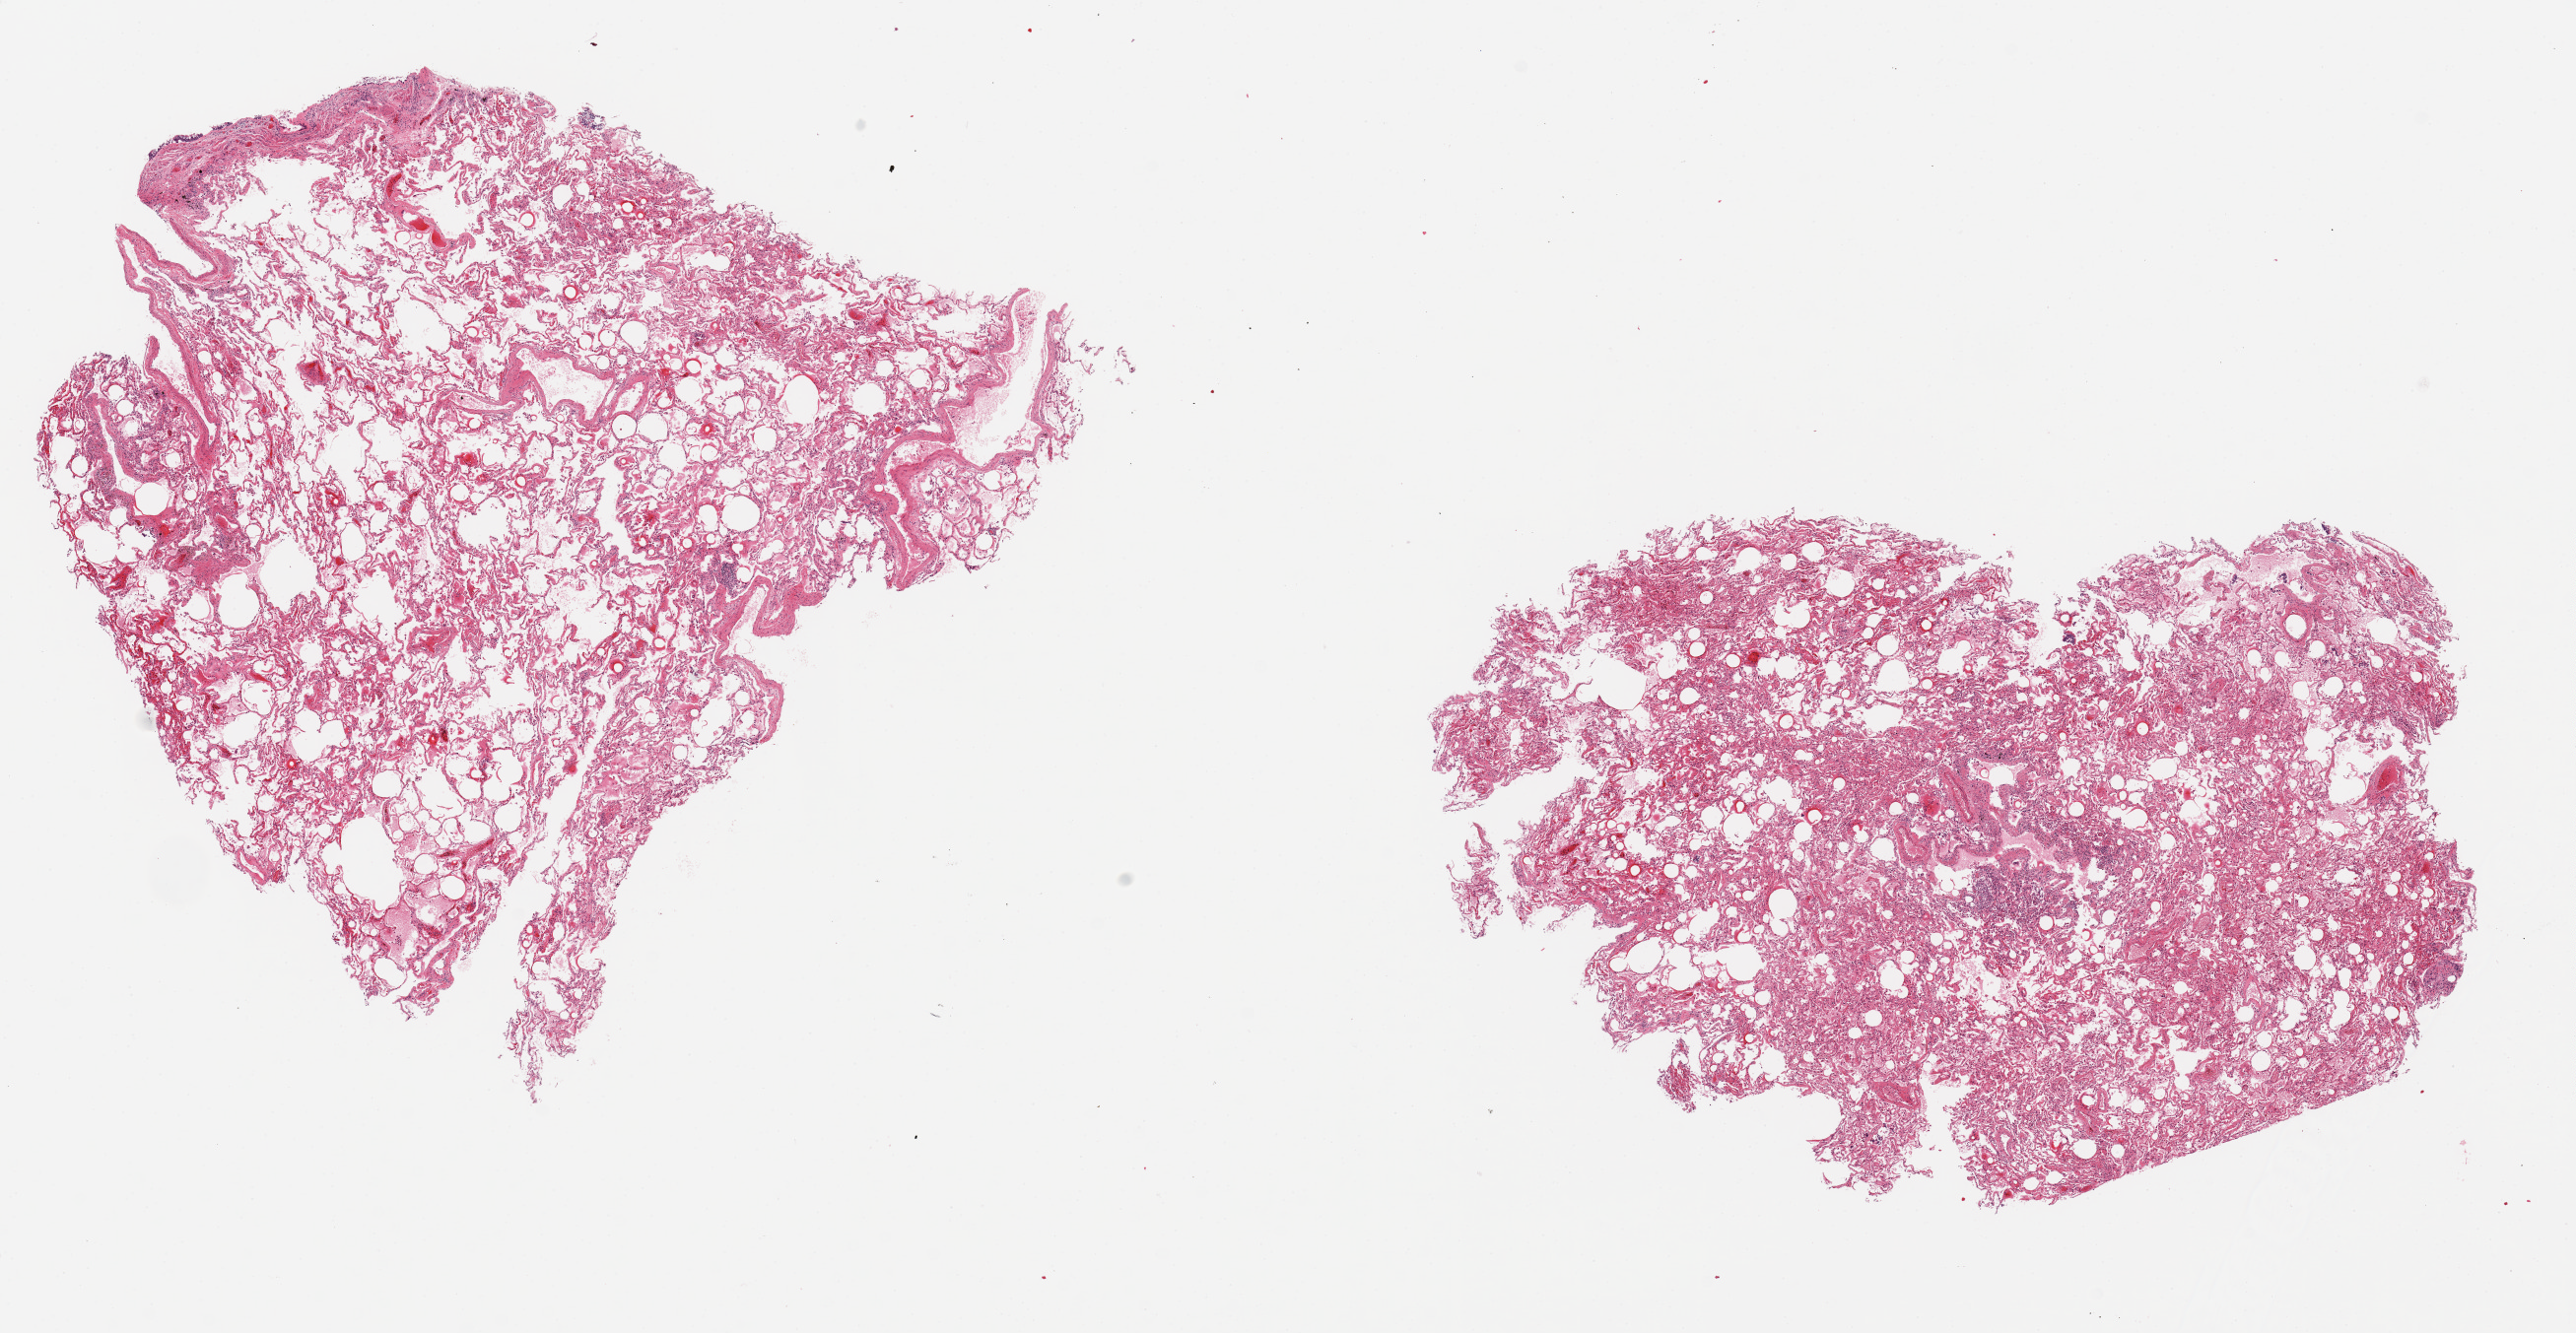
Haematoxylin and eosin whole-slide image — low-resolution overview of the scanned area, about 20.7 x 10.7 mm (acquisition: 20x scan). PAXgene-fixed paraffin-embedded (PFPE) section. Target tissue: lung. Donor tissue sample. Donor: male.
- review note (as recorded): 2 pieces, moderate congestion